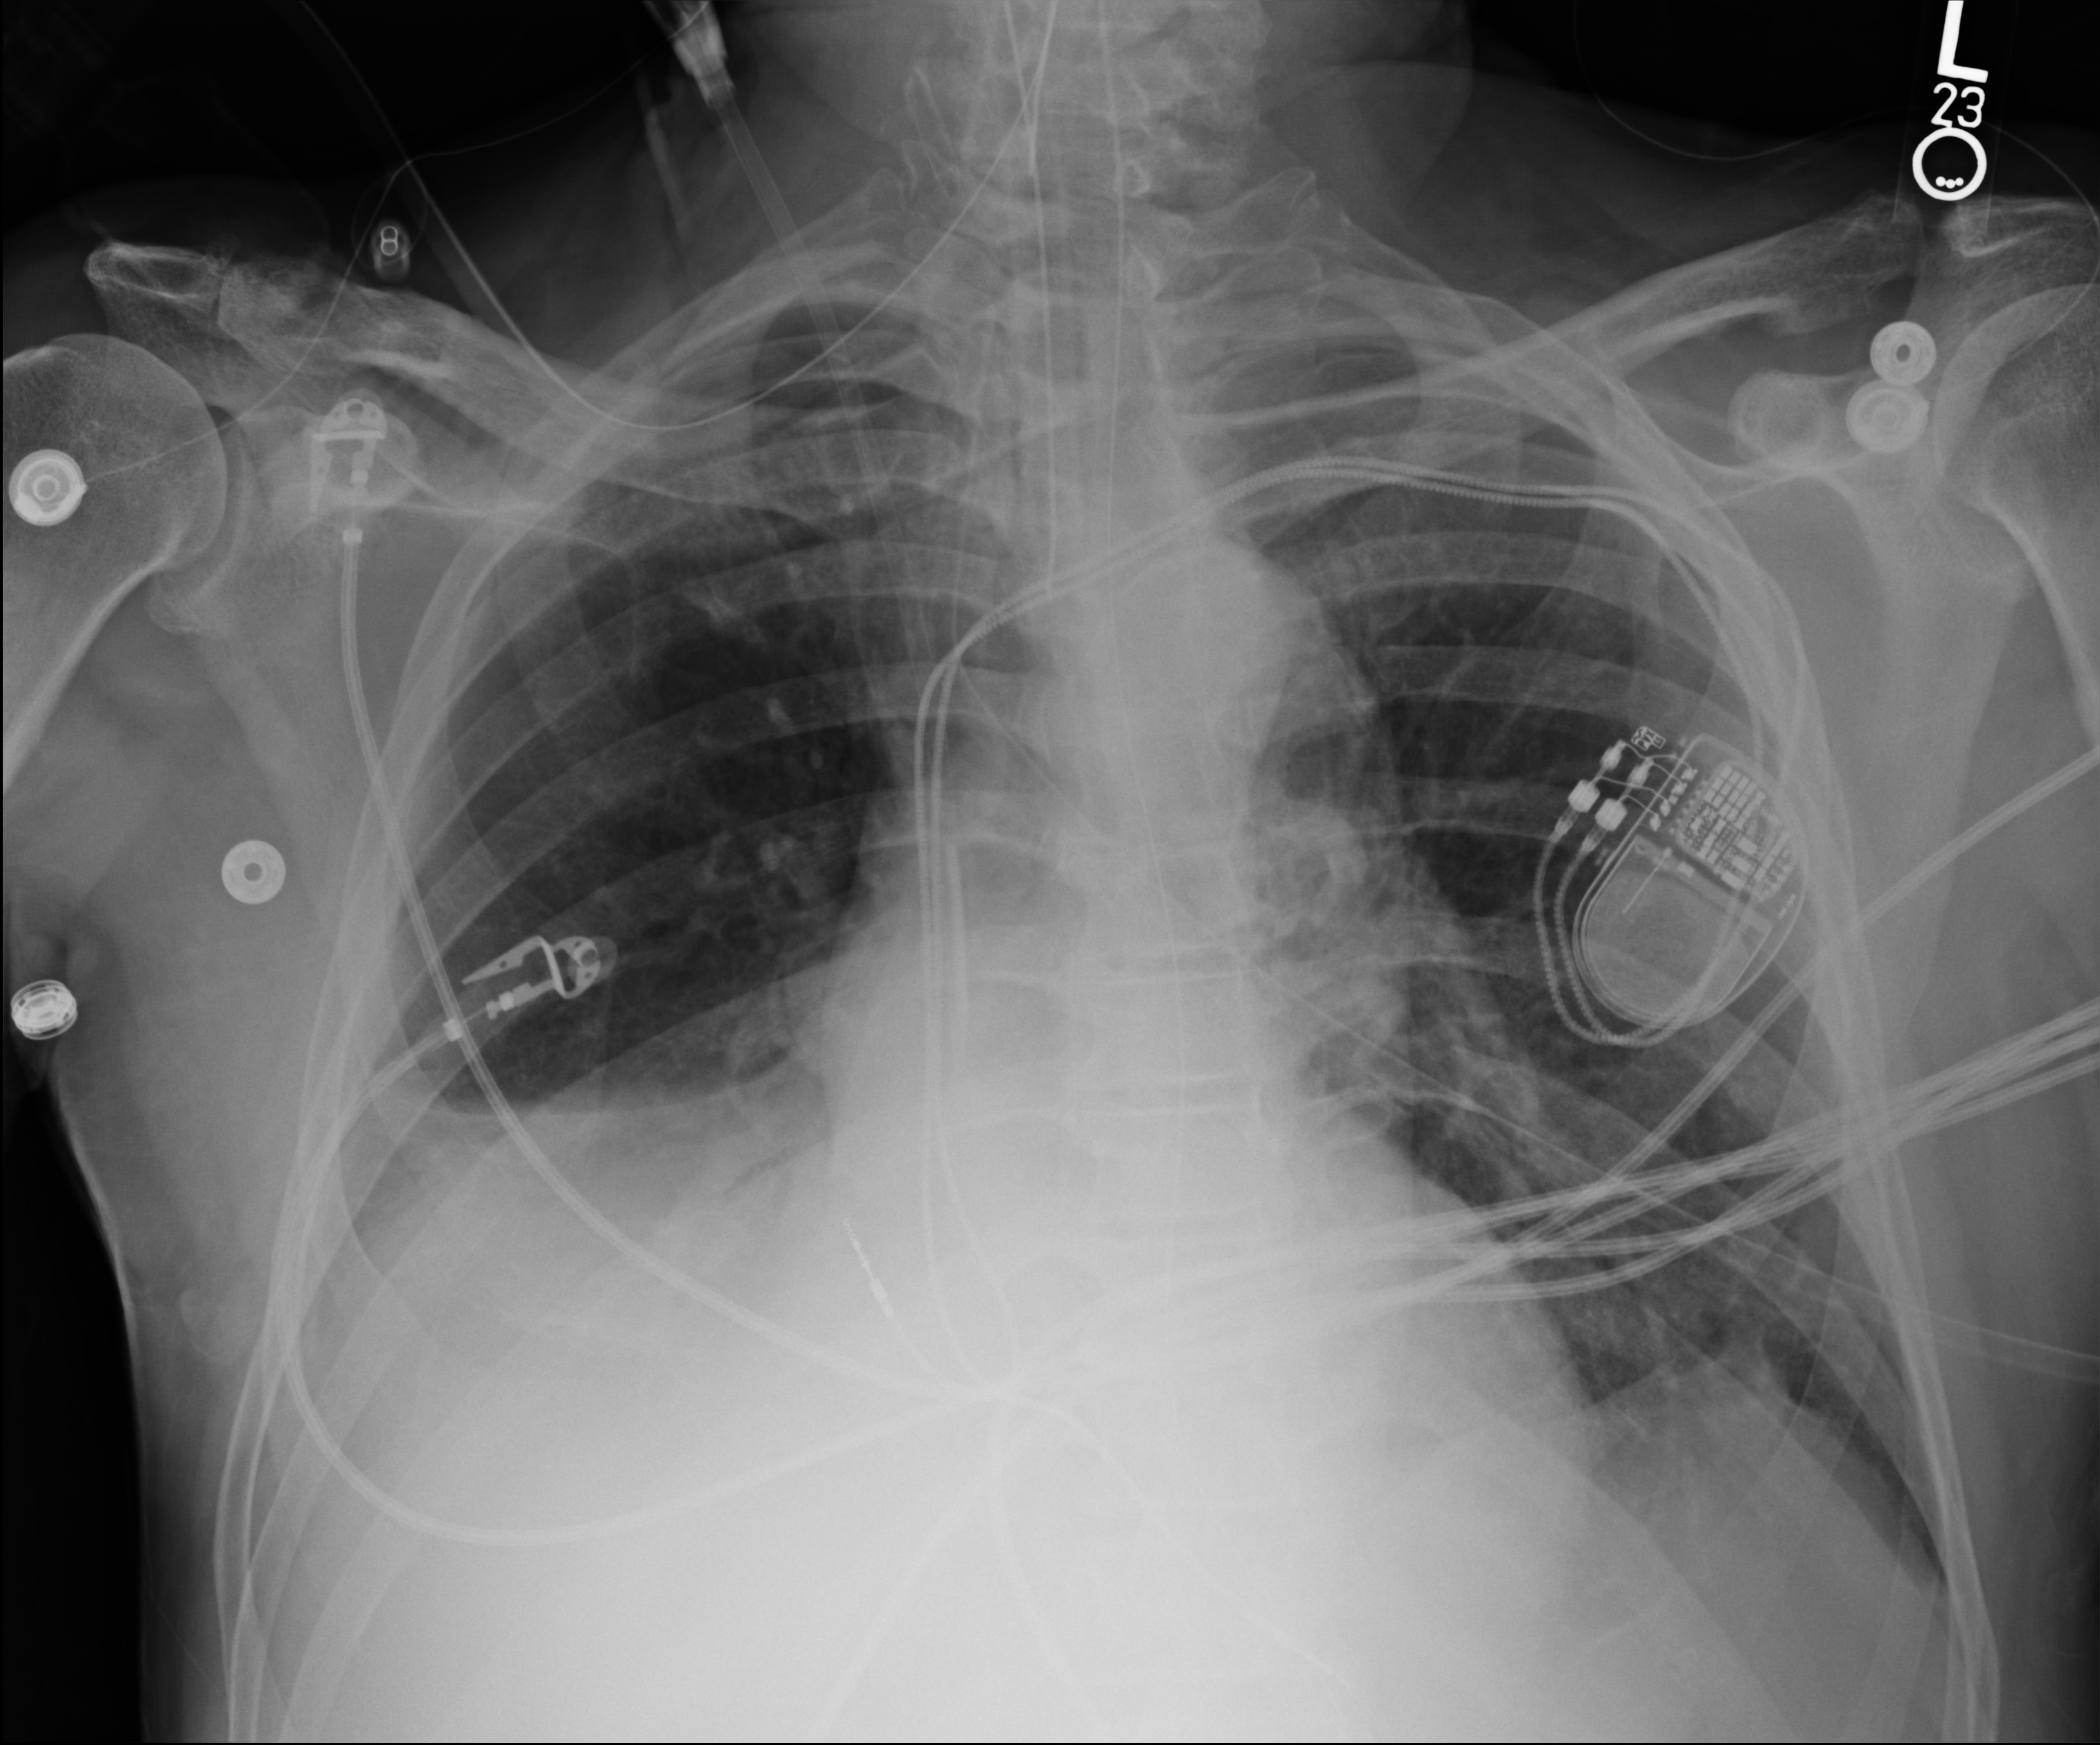
Bedside chest radiograph (computed radiography); anteroposterior (AP) projection. Patient hospitalised with COVID-19; male, aged 60–74 years.
From the hospital-stay record, not from the radiograph (when in the stay this image was taken is not recorded):
- length of hospital stay: 41 days
- mechanically ventilated during this hospital stay: yes